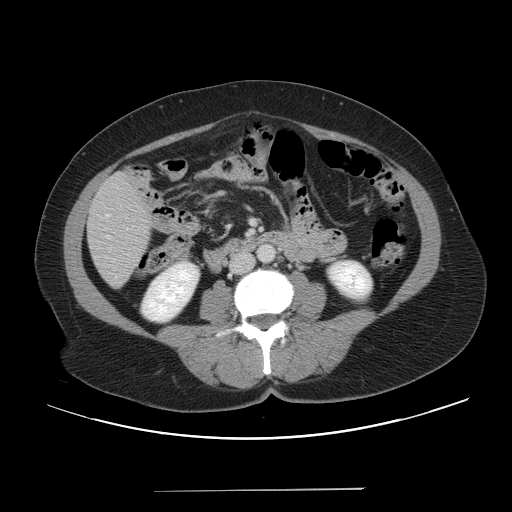
Contrast-enhanced abdominal CT, one axial slice. Position 9 of 56 along the scan axis. Intravenous contrast given. Soft-tissue window (W 400 / L 40 HU). 5 mm slice thickness. 512 × 512 image matrix. Female patient, age 54 years. Case-level facts recorded for this patient, not image findings: diagnosis: colorectal cancer liver metastases, imaged before liver resection; multiple liver metastases: yes; largest metastasis: 3.2 cm; disease in both lobes: yes.
Outlined on this slice (expert manual segmentation):
- liver: bounding box <88,173,152,287> (left, top, right, bottom; pixels)